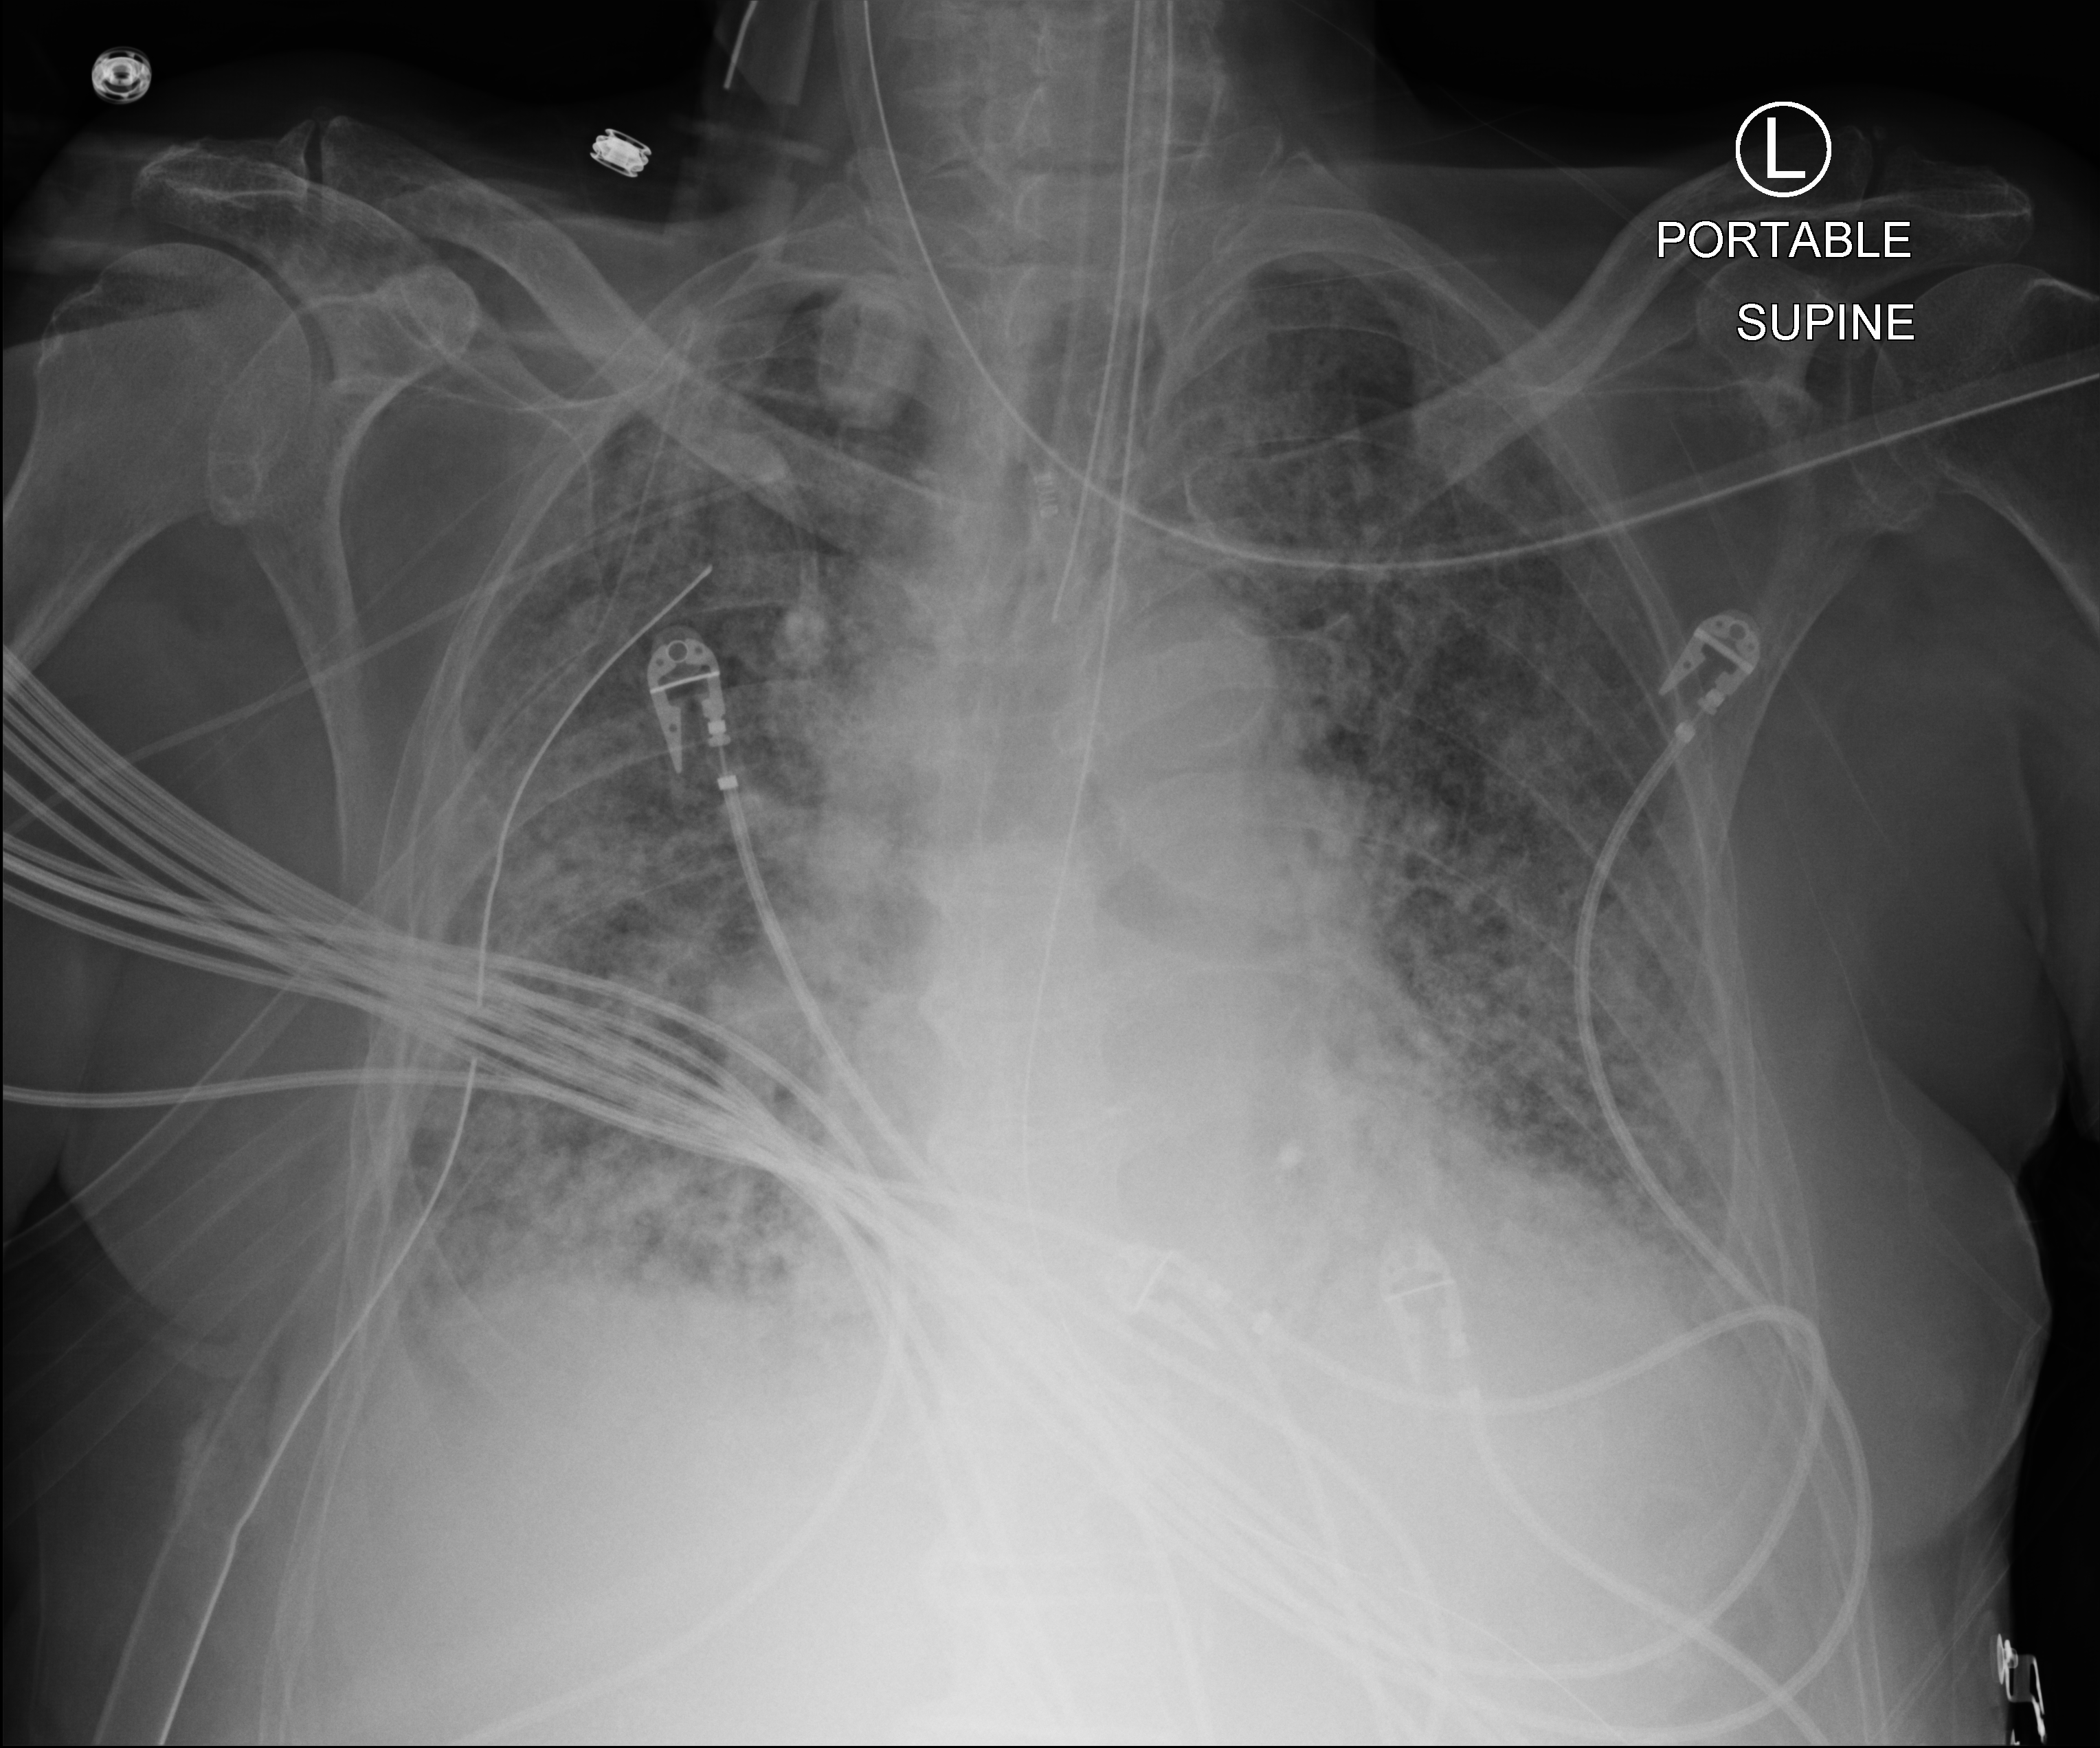
Portable chest radiograph, anteroposterior (AP) projection. Patient hospitalised with COVID-19; male, aged 75–90 years.
Hospital-stay facts (about this admission, not read from this image; timing relative to this image not recorded):
- COPD (admission record): no
- admitted to intensive care during this hospital stay: yes
- mechanically ventilated during this hospital stay: yes